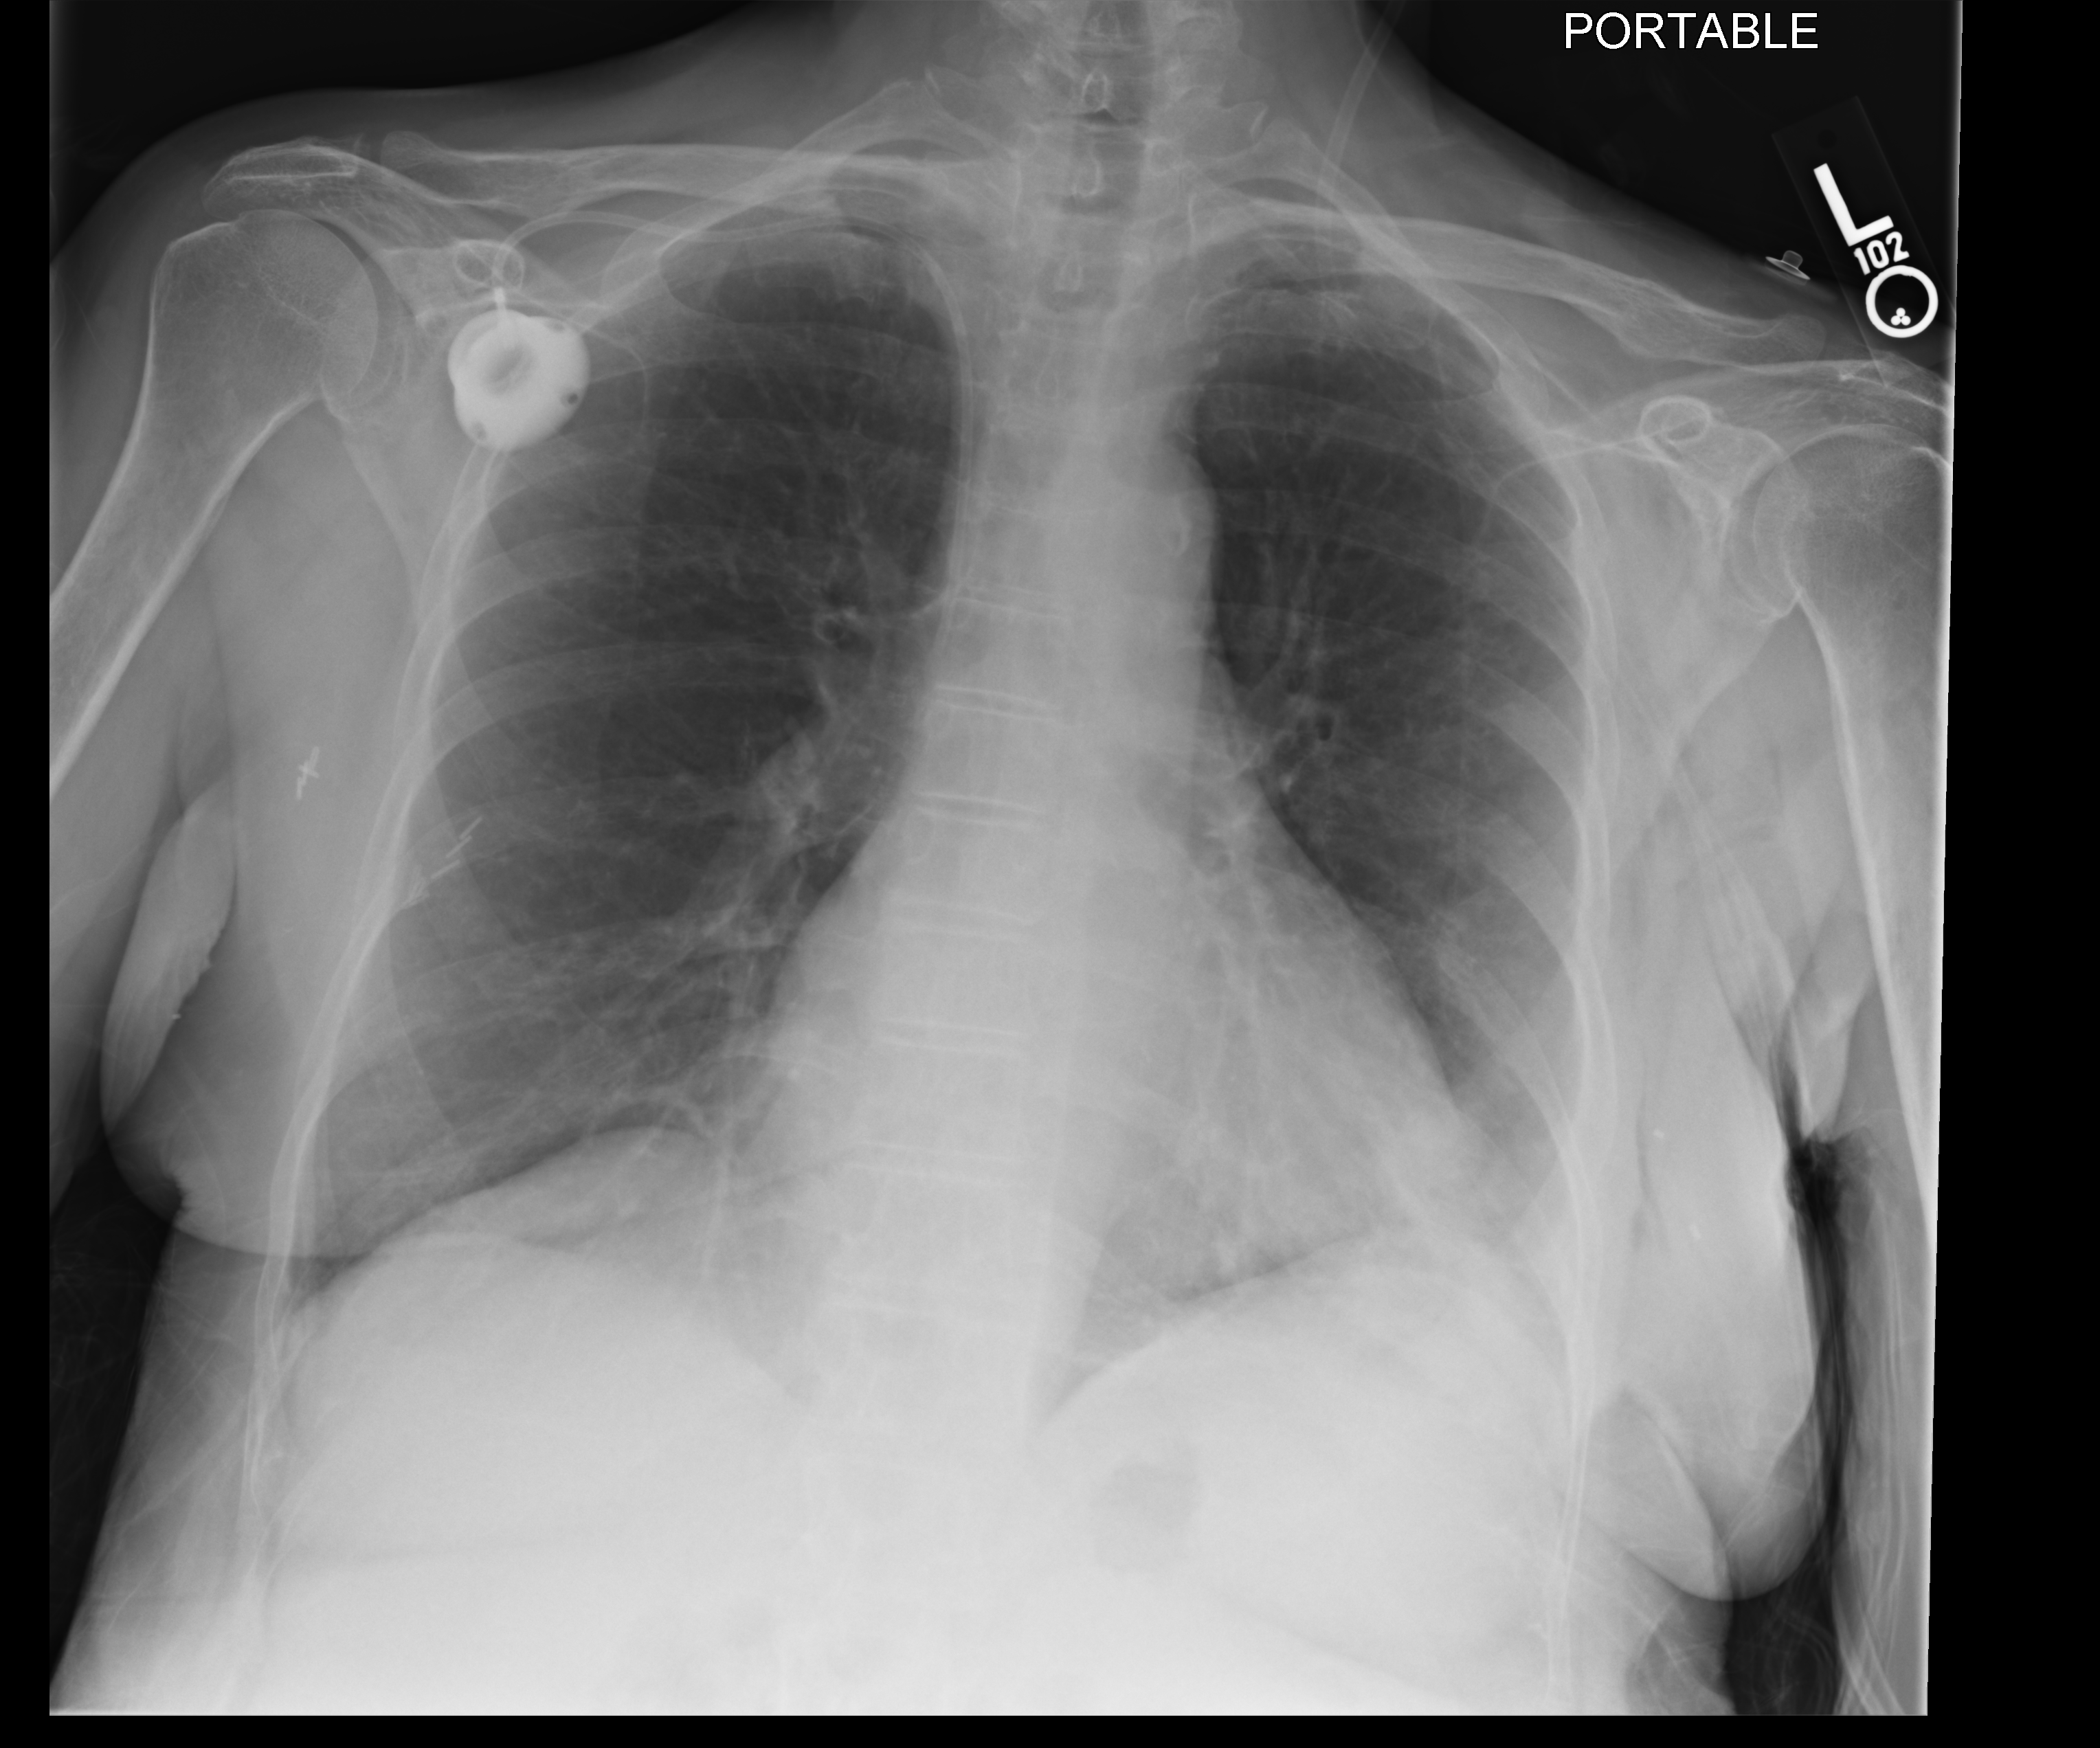
Chest X-ray (portable), anteroposterior (AP) projection. Patient hospitalised with COVID-19; female, aged 60–74 years.
Admission-level facts for this patient (not findings on this image; timing relative to this image not recorded):
- hypertension (admission record): yes